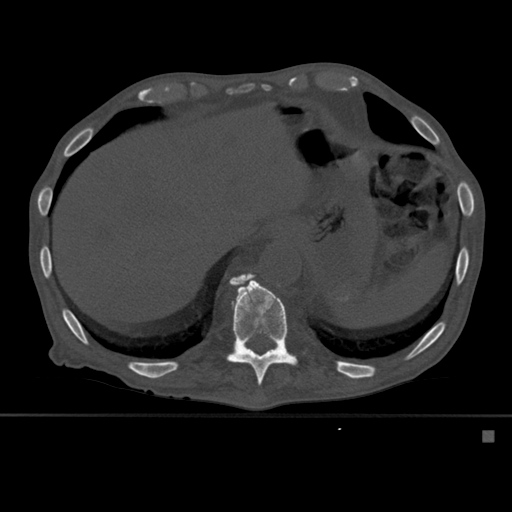
CT including the spine, one axial slice. Slice 296 of 527 in the series (ordered by position). Bone window (W 1800 / L 400 HU). 1.5 mm slice thickness. 512 × 512 image matrix, field of view 373 × 373 mm. Patient: male, 78 years. Case-level facts recorded for this patient, not image findings: primary cancer: prostate.
Structures marked on this image (semi-automatic segmentation, software-assisted and operator-edited):
- T11 vertebra: box from (x=226, y=273) to (x=298, y=386) px